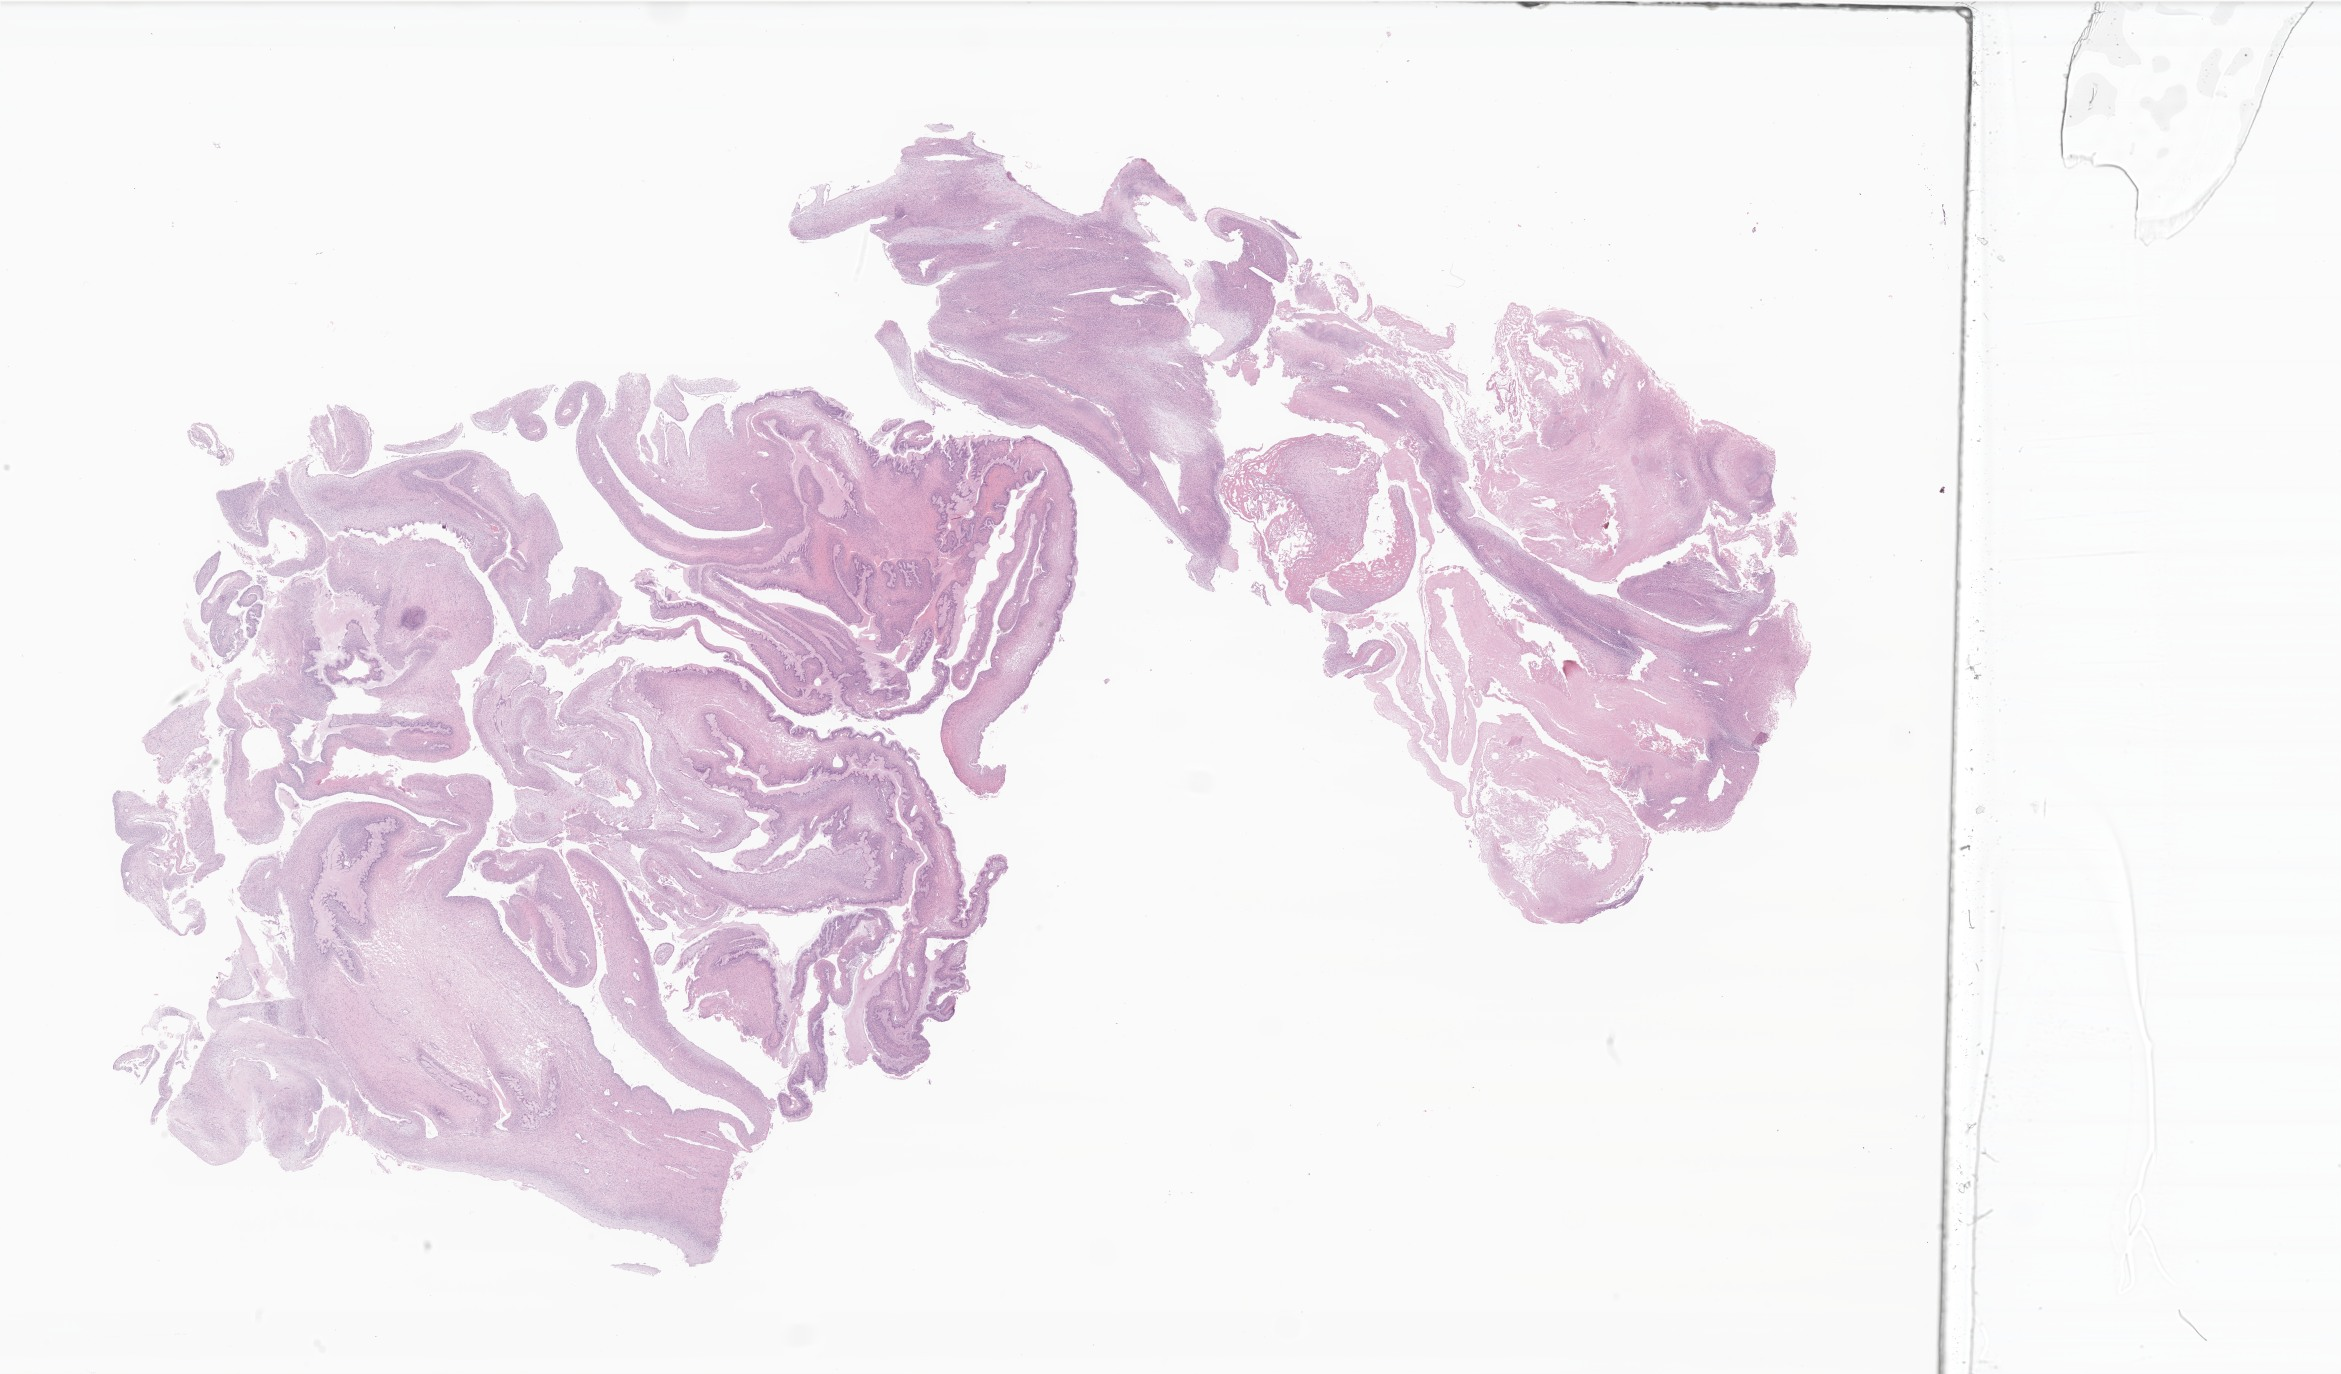
Haematoxylin and eosin whole-slide image of tumor tissue from the ovary, low-resolution overview of the scanned area, about 39.5 x 23.2 mm; formalin-fixed, paraffin-embedded (FFPE) tissue. Patient female; age 312 months (26 years).
Diagnosis: Mucinous cystic tumor of borderline malignancy.